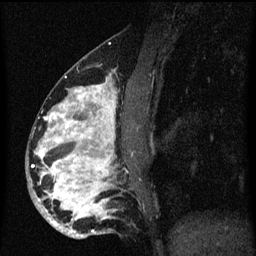
Breast MRI (dynamic contrast-enhanced), one sagittal slice. Position 26 of 60 along the scan axis. Dynamic contrast-enhanced series, image 2 of 3 at this slice position (ordered by acquisition). 1.5 T. TE 4.2 ms, TR 8.4 ms. 2 mm slice thickness. 256 × 256 image matrix. Female patient, age 34 years. From the clinical record (not read from this slice): setting: breast cancer imaged before/during neoadjuvant chemotherapy; receptor status: HR-positive, HER2-negative.
Annotated regions visible in this slice (semi-automatically segmented with operator editing):
- analysis volume of interest (the breast-tissue region the enhancement analysis was run in; not a lesion): bounding box <26,58,137,239> (left, top, right, bottom; pixels)
- tumour enhancement mask (voxels above the 70 % enhancement threshold inside the analysis volume of interest): <36,78,117,233>